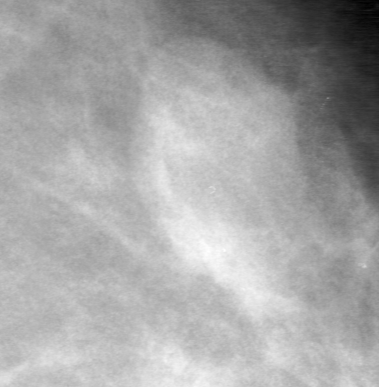
Cropped region of a digitized screen-film mammogram centred on a radiologist-marked abnormality, left breast, MLO view, BI-RADS breast density category 2 (scale 1–4).
Finding: mass, shape lobulated, margins obscured; BI-RADS assessment category 0 (incomplete: needs additional imaging); subtlety rating 4 on a 1 (subtle) to 5 (obvious) scale; pathology (as recorded): benign.